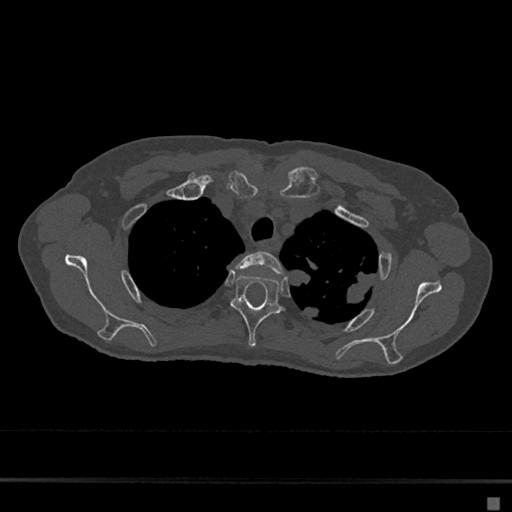
CT including the spine, one axial slice; position 542 of 797 along the scan axis; reconstruction kernel Br40s/3; bone window (W 1800 / L 400 HU); 0.5 mm slice thickness; 512 × 512 image matrix, field of view 360 × 360 mm. Patient: female, 68 years. From the clinical record (not read from this slice): primary cancer: renal.
Structures marked on this image (semi-automatically segmented with operator editing):
- T2 vertebra: bounding box [x1, y1, x2, y2] px = [236, 251, 284, 275]
- T3 vertebra: [231, 275, 282, 347]